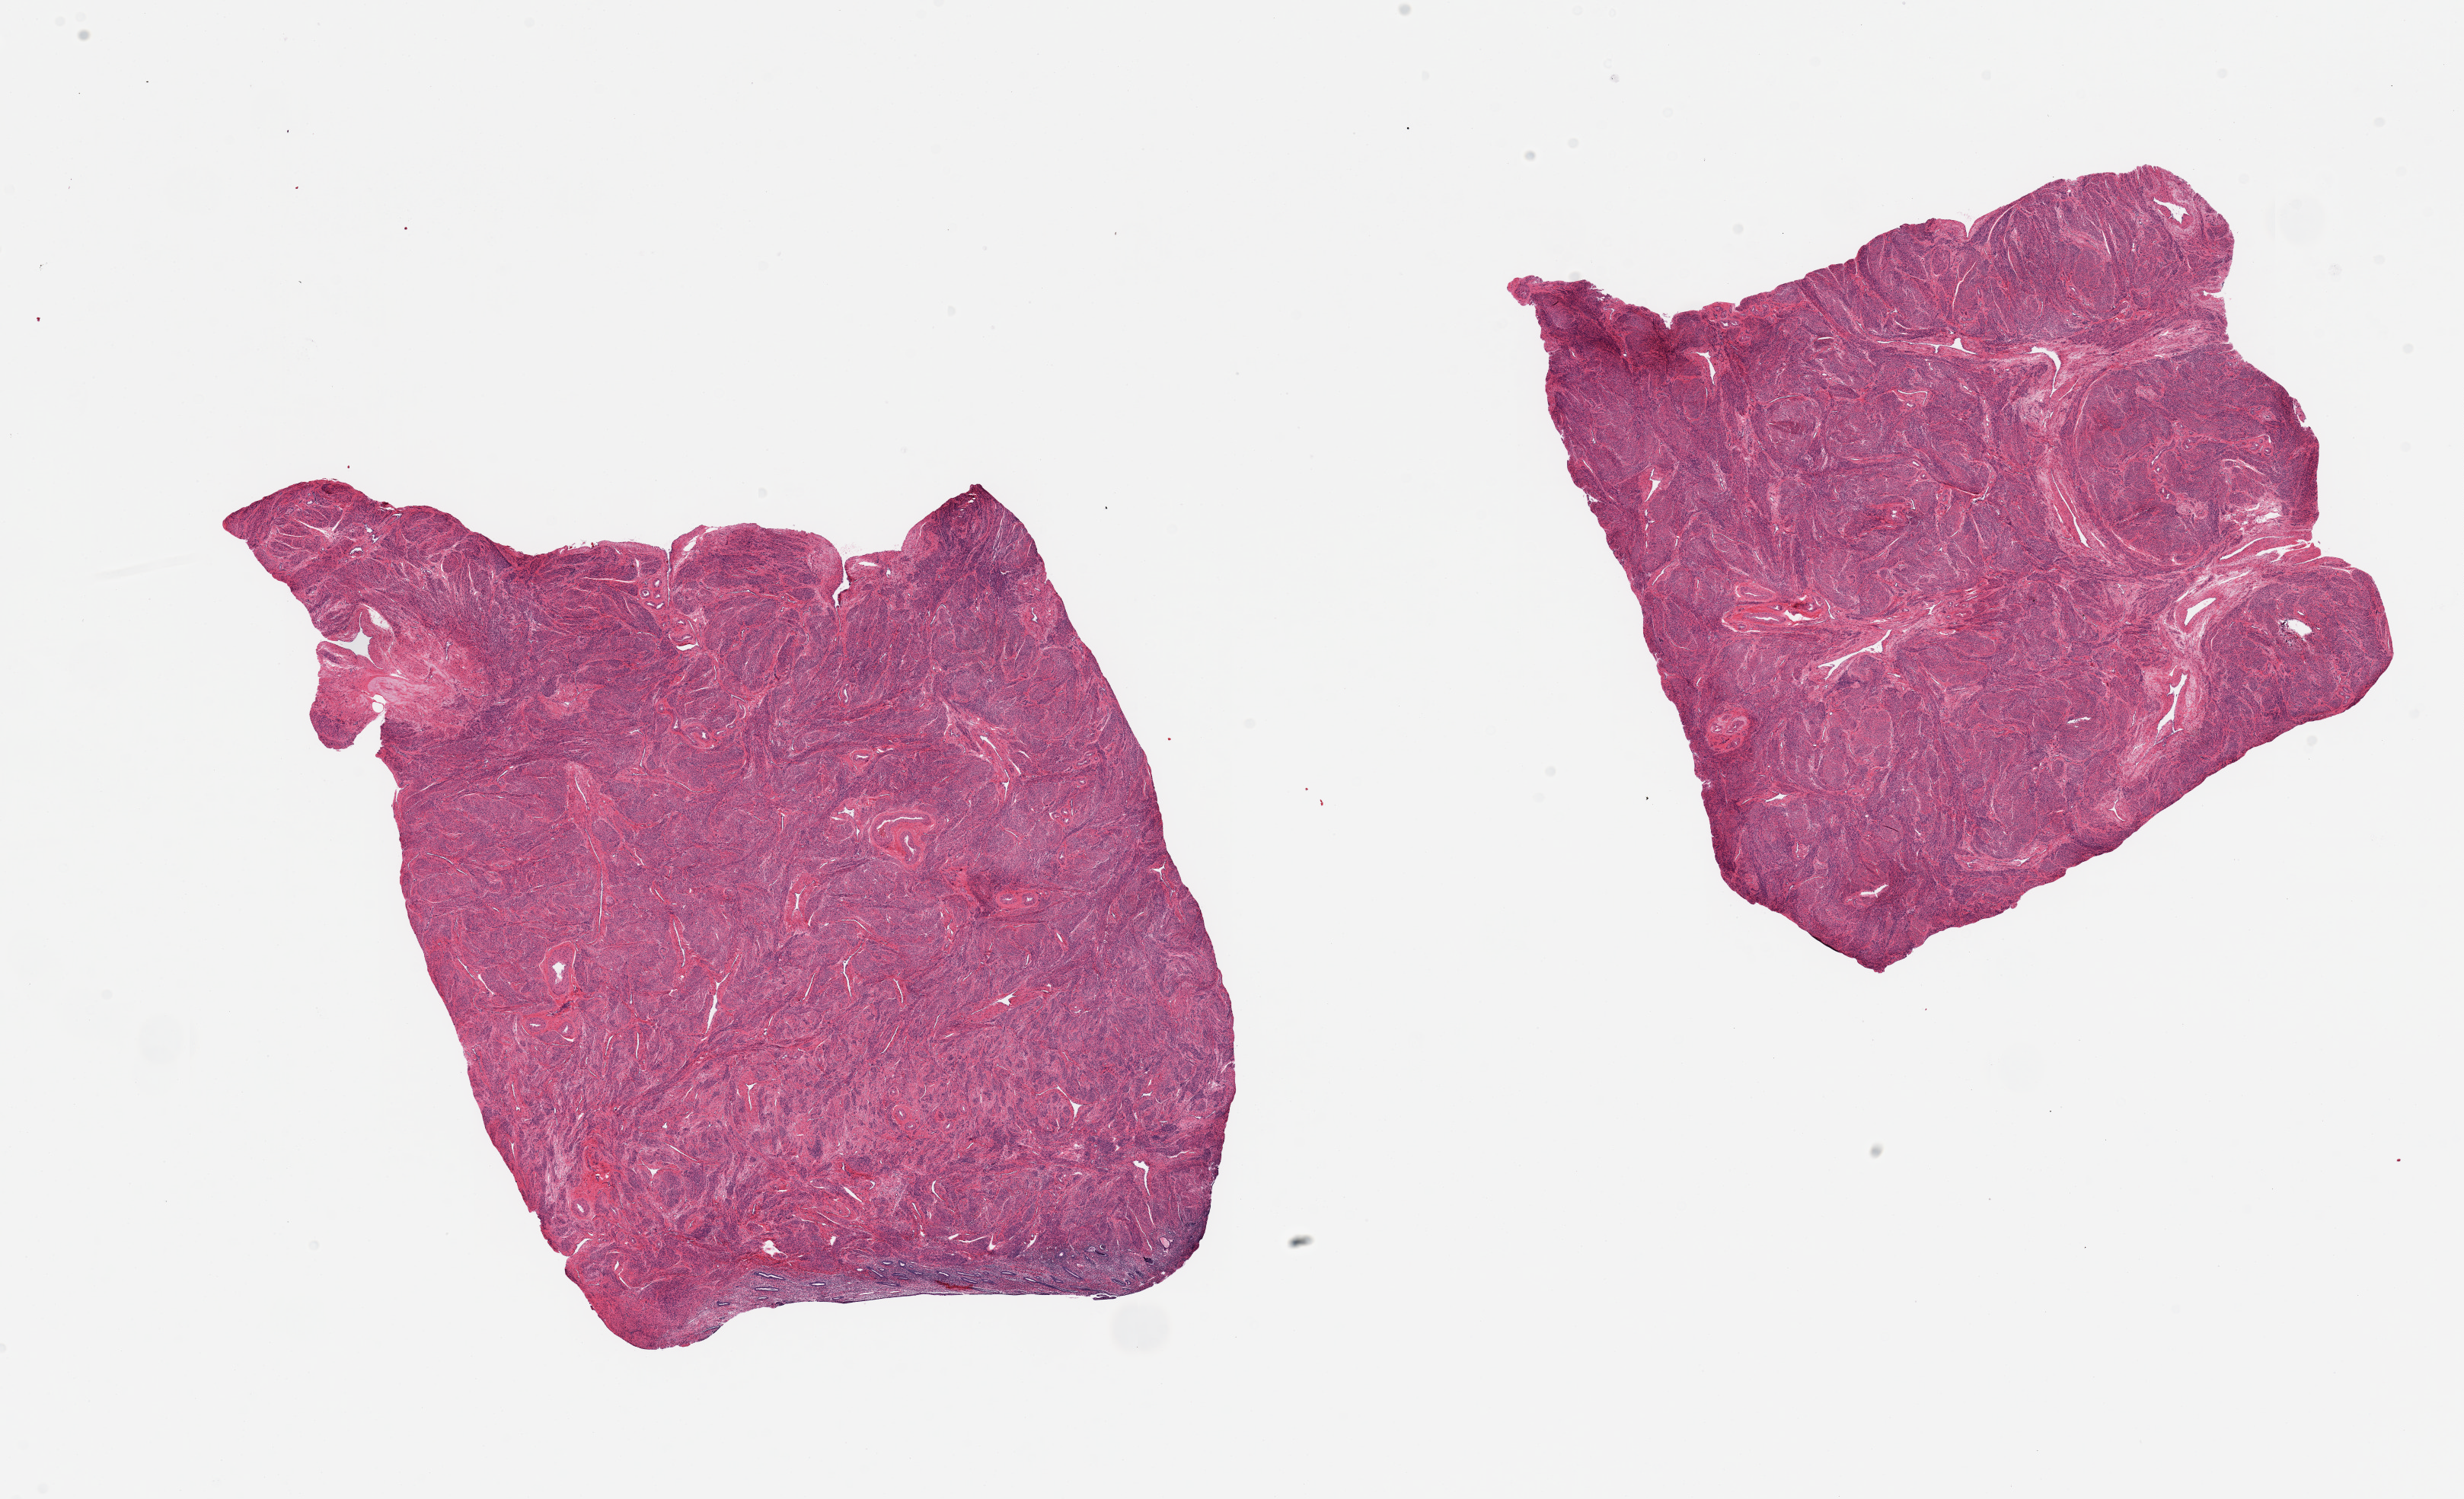
Digitized hematoxylin and eosin (H&E)-stained section — a low-resolution overview of the entire scanned area, about 25.6 x 15.6 mm (slide scanned at 20x), PAXgene-fixed, paraffin-embedded tissue, sampled site (target tissue): uterus, tissue donor sample.
• reviewer comment on this tissue sample: 2 pieces; thin endometrium on one